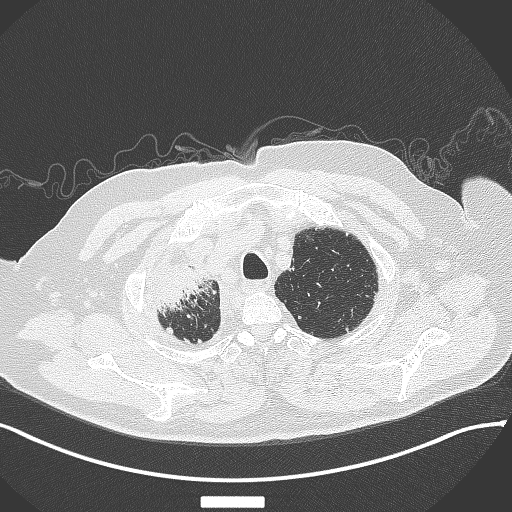
Chest CT, one axial slice; slice 321 of 384 in the series (ordered by position); reconstruction kernel B70f; lung window (W 1500 / L -600 HU); 512 × 512 image matrix. Patient: male, 69 years. From the clinical record (not read from this slice): clinical TNM (as recorded): T4 N3 M1.
Outlined on this slice (bounding box drawn by a radiologist):
- lung tumour (recorded histology: adenocarcinoma): bounding box [x1, y1, x2, y2] px = [150, 257, 215, 321]